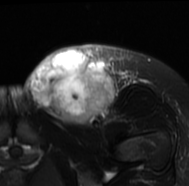
MRI of an extremity soft-tissue mass, one axial slice. Slice 41 of 77 in the series (ordered by position). T2-weighted fat-saturated. MR volume resampled by the dataset authors to the PET/CT grid (not the native acquisition matrix). 3.27 mm slice thickness. 189 × 186 image matrix, field of view 185 × 182 mm. Female patient. Case-level facts recorded for this patient, not image findings: histological type: leiomyosarcoma; grade: high; site of the primary tumour: groin.
Outlined on this slice (expert contour drawn on MRI and transferred to this co-registered scan by the dataset authors):
- gross tumour volume including surrounding oedema: bounding box (x1, y1, x2, y2) in pixels: (24, 43, 137, 128)
- gross tumour volume (mass): (29, 49, 116, 126)